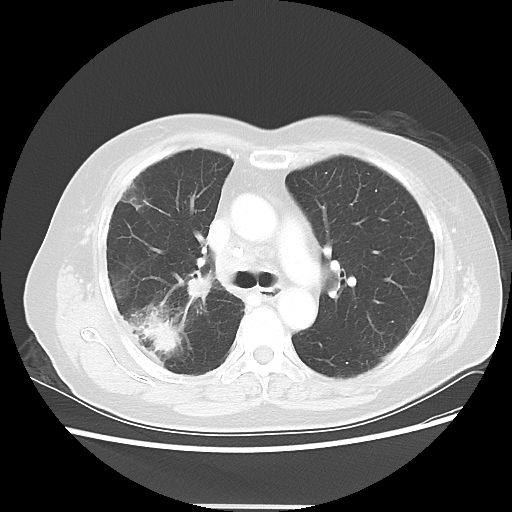
Chest CT, one axial slice; position 31 of 50 along the scan axis; reconstruction kernel LUNG; 120 kVp; lung window (W 1500 / L -600 HU); 5 mm slice thickness; 512 × 512 image matrix, field of view 360 × 360 mm. Female patient, age 72 years. Case-level facts recorded for this patient, not image findings: clinical TNM (as recorded): T2 N1 M0.
Outlined on this slice (rectangle marked by the reading radiologist):
- lung tumour (recorded histology: adenocarcinoma): bounding box (x1, y1, x2, y2) in pixels: (135, 307, 180, 355)